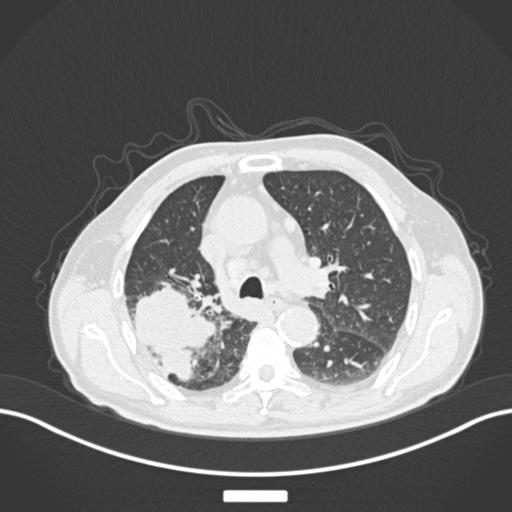
Chest CT, one axial slice. Slice 120 of 201 in the series (ordered by position). Reconstruction kernel B30f. 120 kVp. Lung window (W 1500 / L -600 HU). 512 × 512 image matrix. Male patient, age 72 years. From the clinical record (not read from this slice): clinical TNM (as recorded): T3 N2 M0.
Outlined on this slice (bounding box drawn by a radiologist):
- lung tumour (recorded histology: adenocarcinoma): bounding box (x1, y1, x2, y2) in pixels: (134, 281, 220, 382)